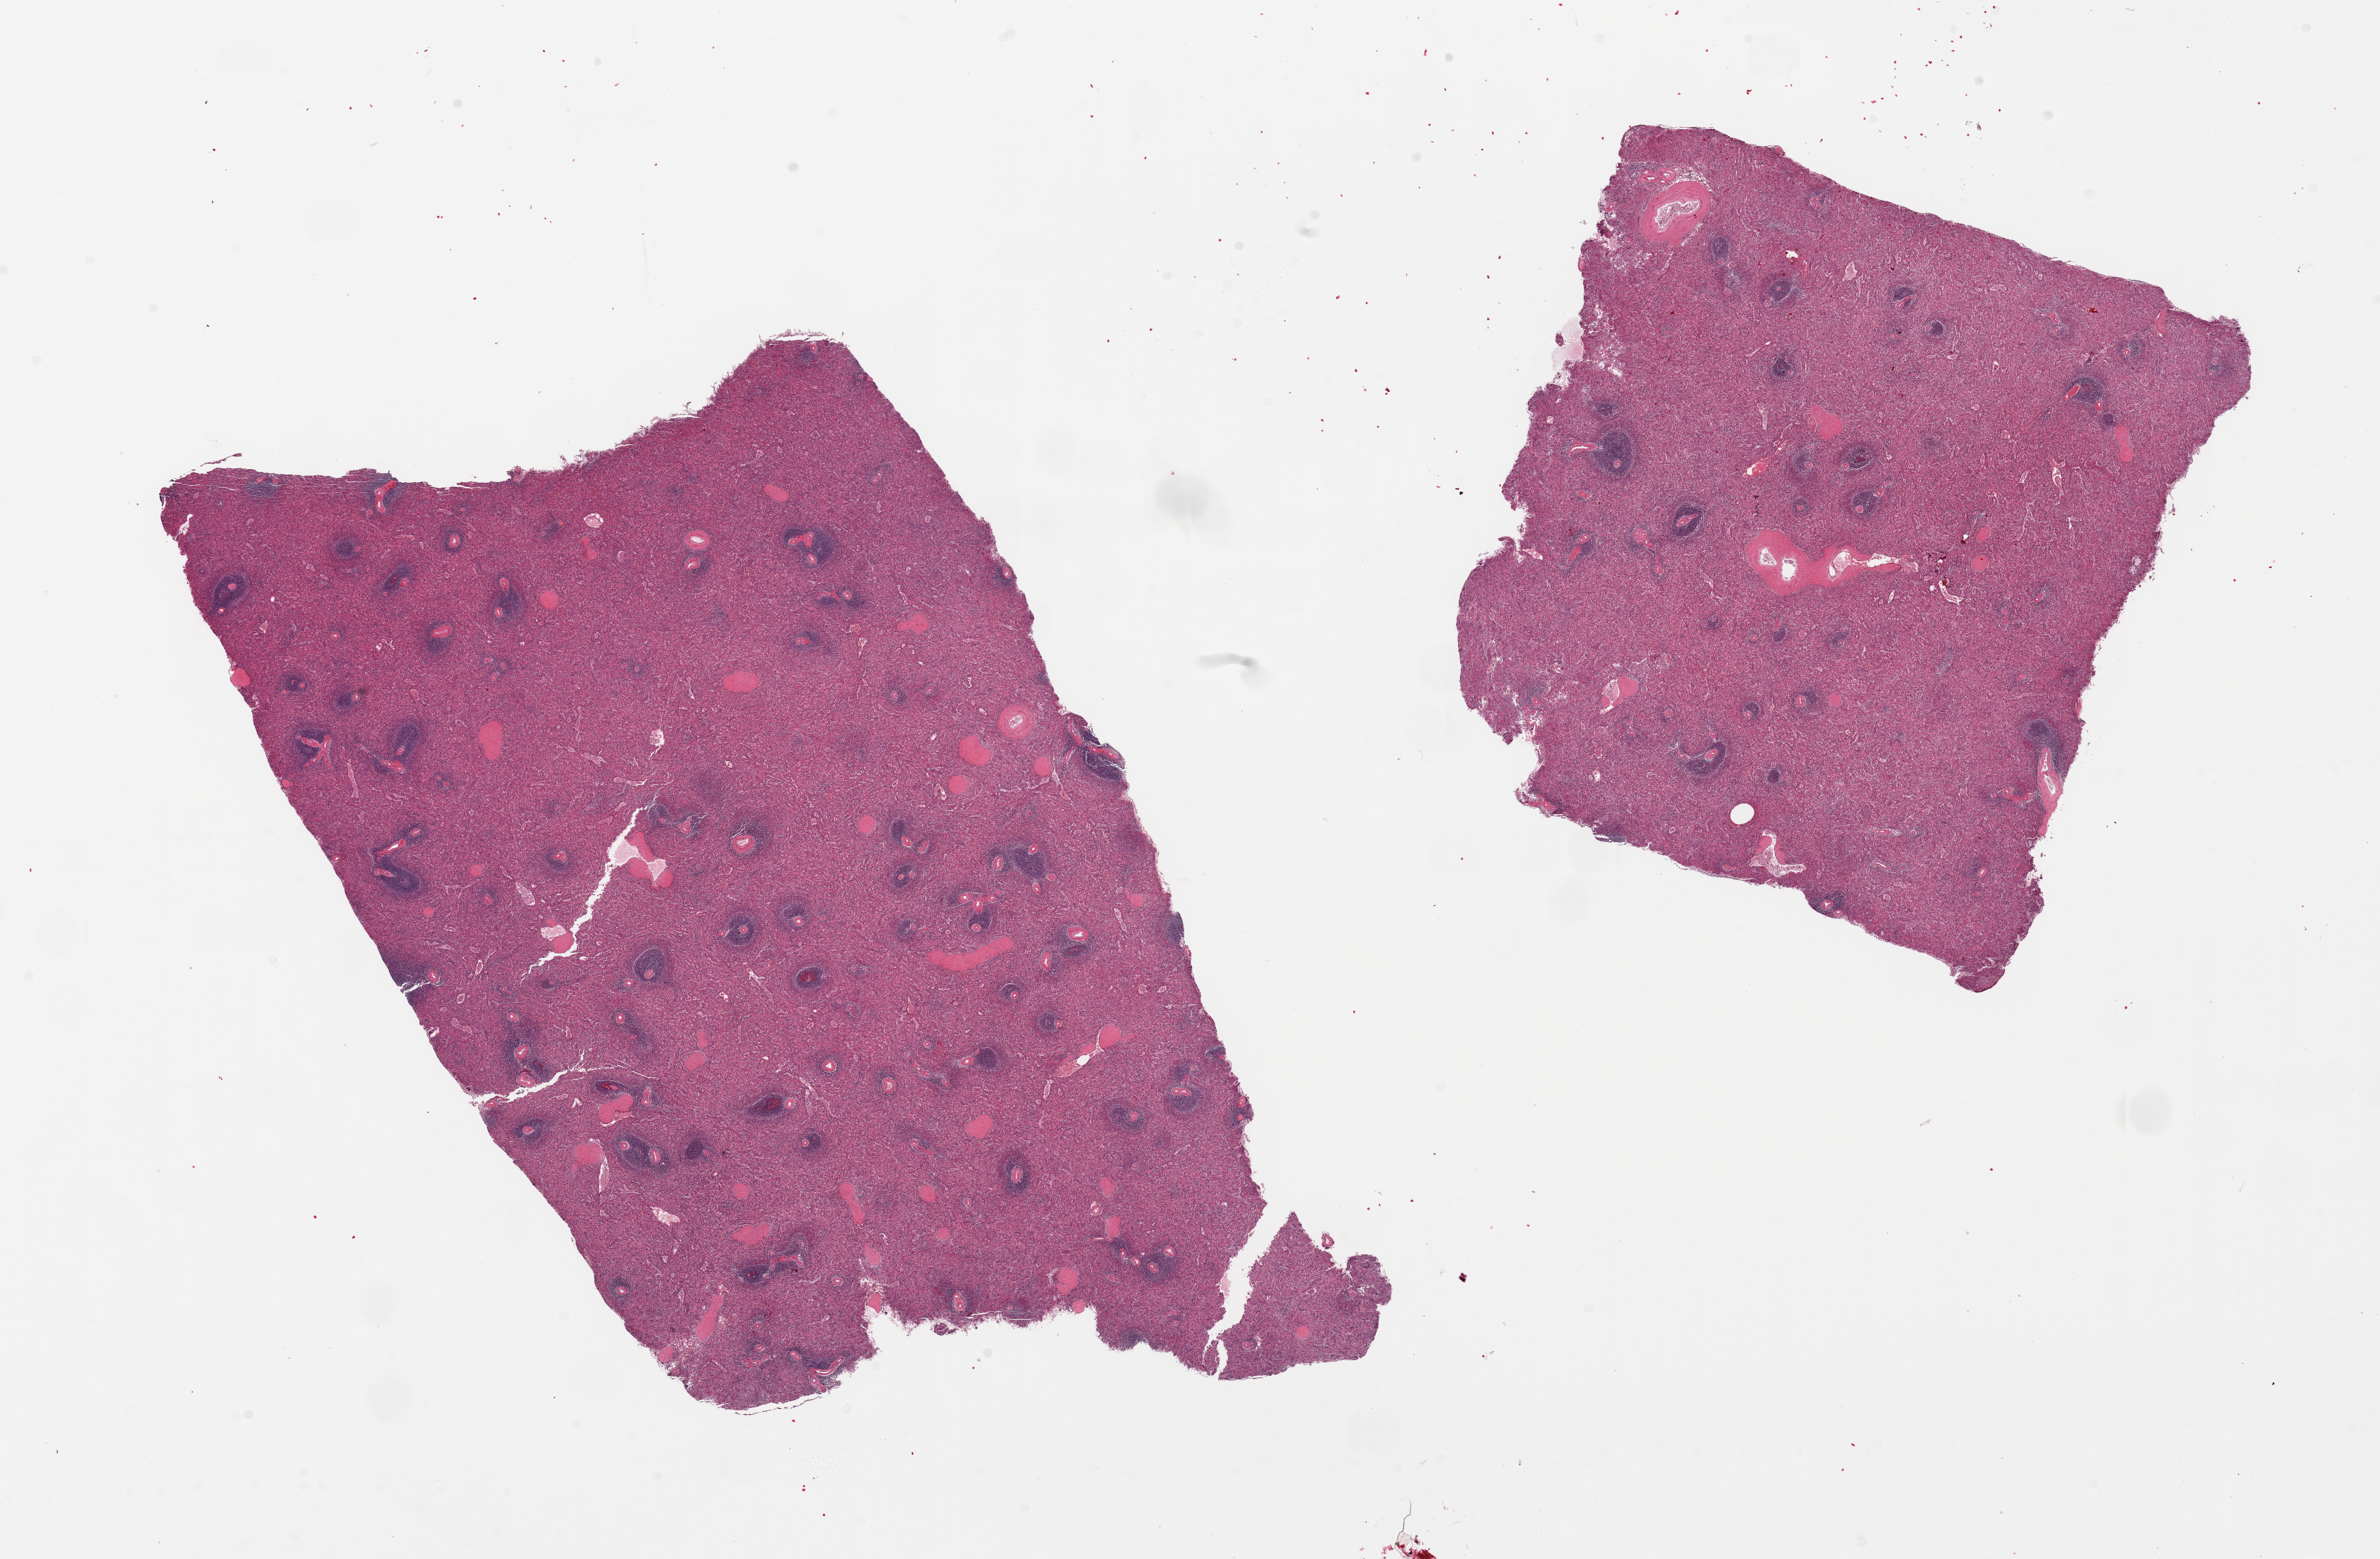
Whole-slide image, haematoxylin and eosin stain — low-resolution overview of the scanned area, about 27.6 x 18.1 mm. PAXgene-fixed paraffin-embedded (PFPE) section. Section of spleen (target tissue). Donor tissue sample. Donor: male.
• review note (as recorded): 2 pieces